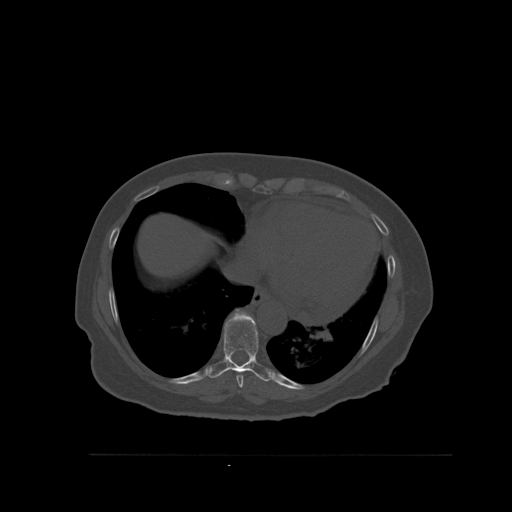
CT including the spine, one axial slice. Slice 337 of 527 in the series (ordered by position). Bone window (W 1800 / L 400 HU). 1.5 mm slice thickness. 512 × 512 image matrix, field of view 470 × 470 mm. Patient: female, 73 years. Case-level facts recorded for this patient, not image findings: primary cancer: breast; vertebrae with lytic lesions (as recorded): L2.
Structures marked on this image (semi-automatic segmentation, software-assisted and operator-edited):
- T8 vertebra: bounding box <236,375,244,388> (left, top, right, bottom; pixels)
- T9 vertebra: <209,309,273,382>